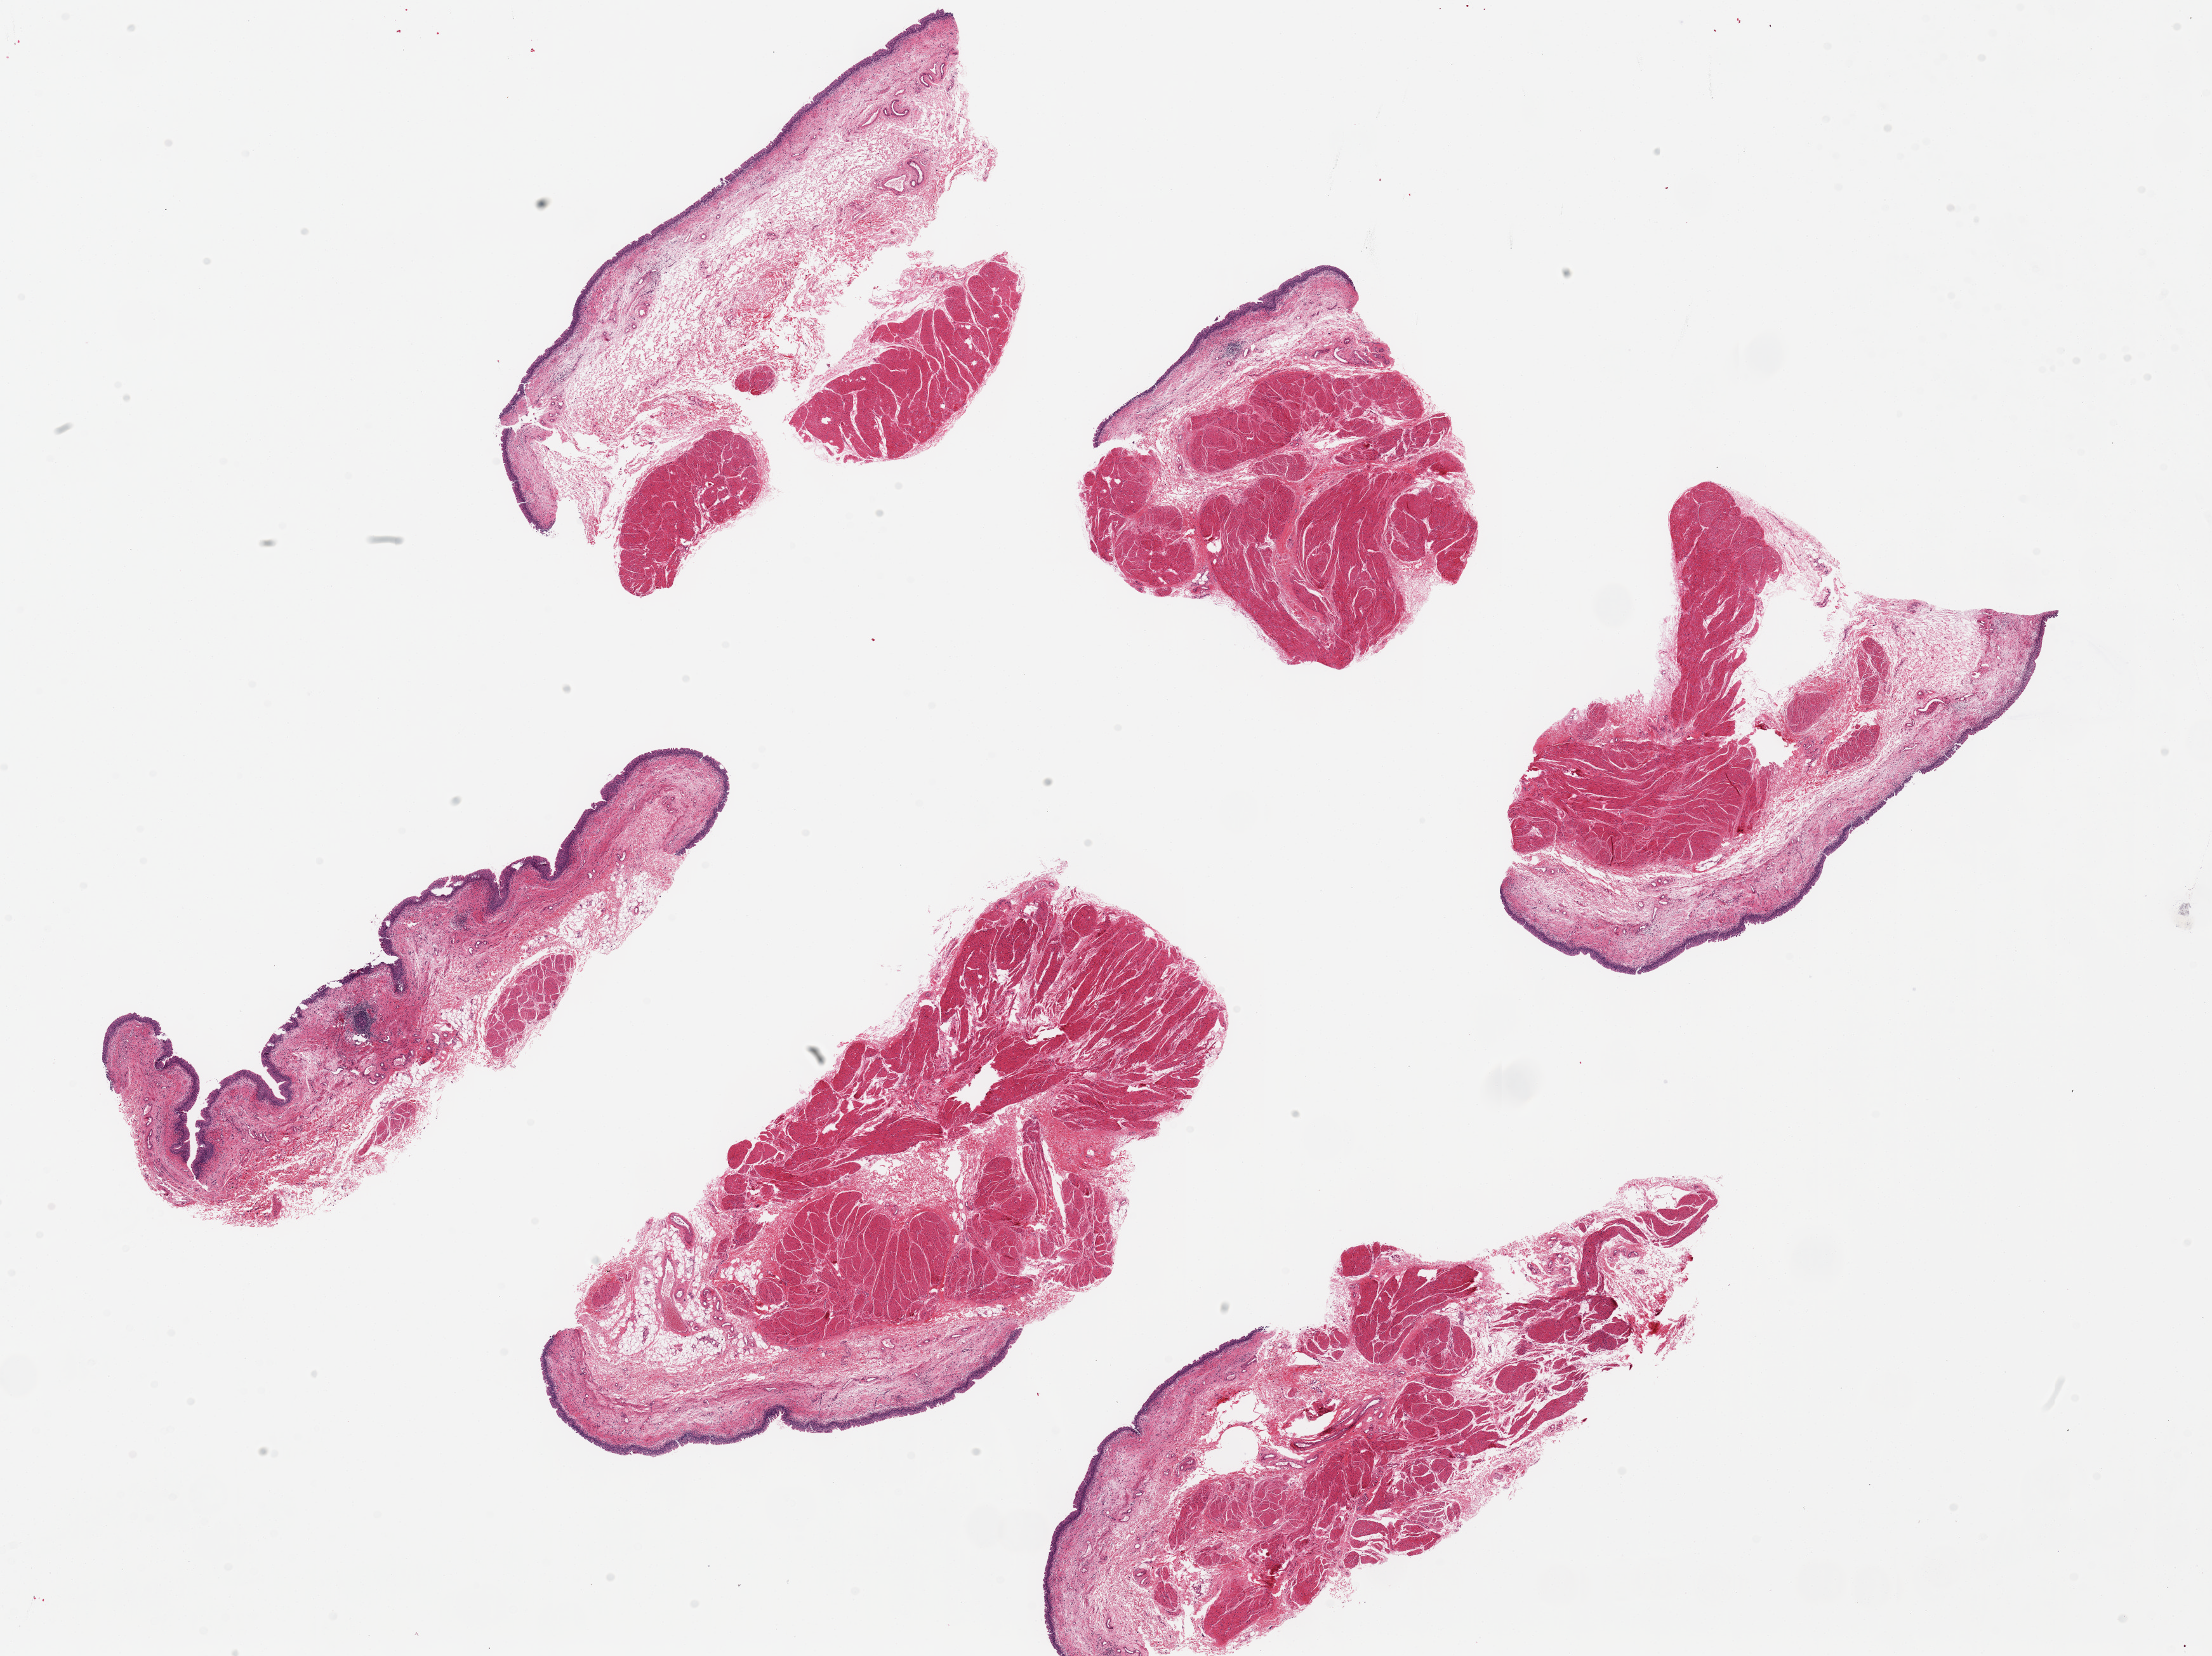
Whole-slide image, H&E stain, brightfield — low-resolution overview of the scanned area, about 27.6 x 20.6 mm (from a 20x scan). PAXgene-fixed paraffin-embedded (PFPE) section. Sampled site (target tissue): urinary bladder. Donor tissue sample.
- reviewer comment on this tissue sample: 6 pieces up to 9x4 mm; all with epithelium up to 0.1 mm thick